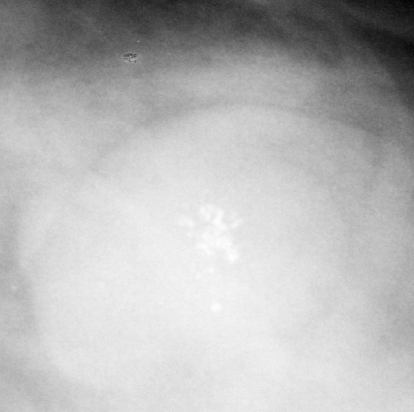
Cropped region of a digitized screen-film mammogram centred on a radiologist-marked abnormality, left breast, CC view, BI-RADS breast density category 3 (scale 1–4).
Mass, shape lobulated, margins obscured; BI-RADS assessment category 3; pathology result (as recorded, not read from the image): benign.